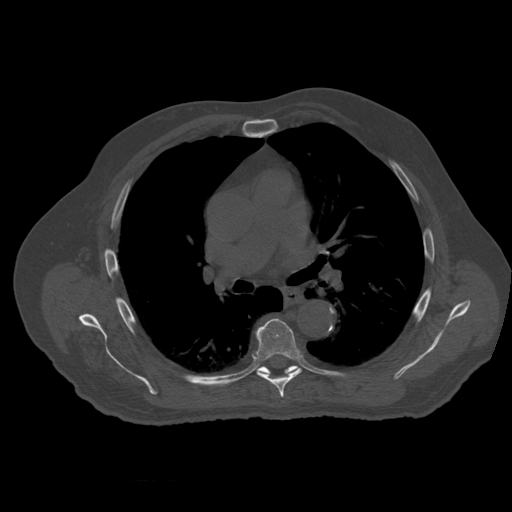
CT including the spine, one axial slice. Slice 376 of 399 in the series (ordered by position). 120 kVp. Bone window (W 1800 / L 400 HU). 1.25 mm slice thickness. 512 × 512 image matrix, field of view 407 × 407 mm. Patient age 73 years. From the clinical record (not read from this slice): primary cancer: prostate; vertebrae with lytic lesions (as recorded): L2.
Annotated regions visible in this slice (semi-automatically segmented with operator editing):
- T6 vertebra: box from (x=256, y=319) to (x=302, y=398) px
- T7 vertebra: (x=259, y=366)–(x=298, y=375)